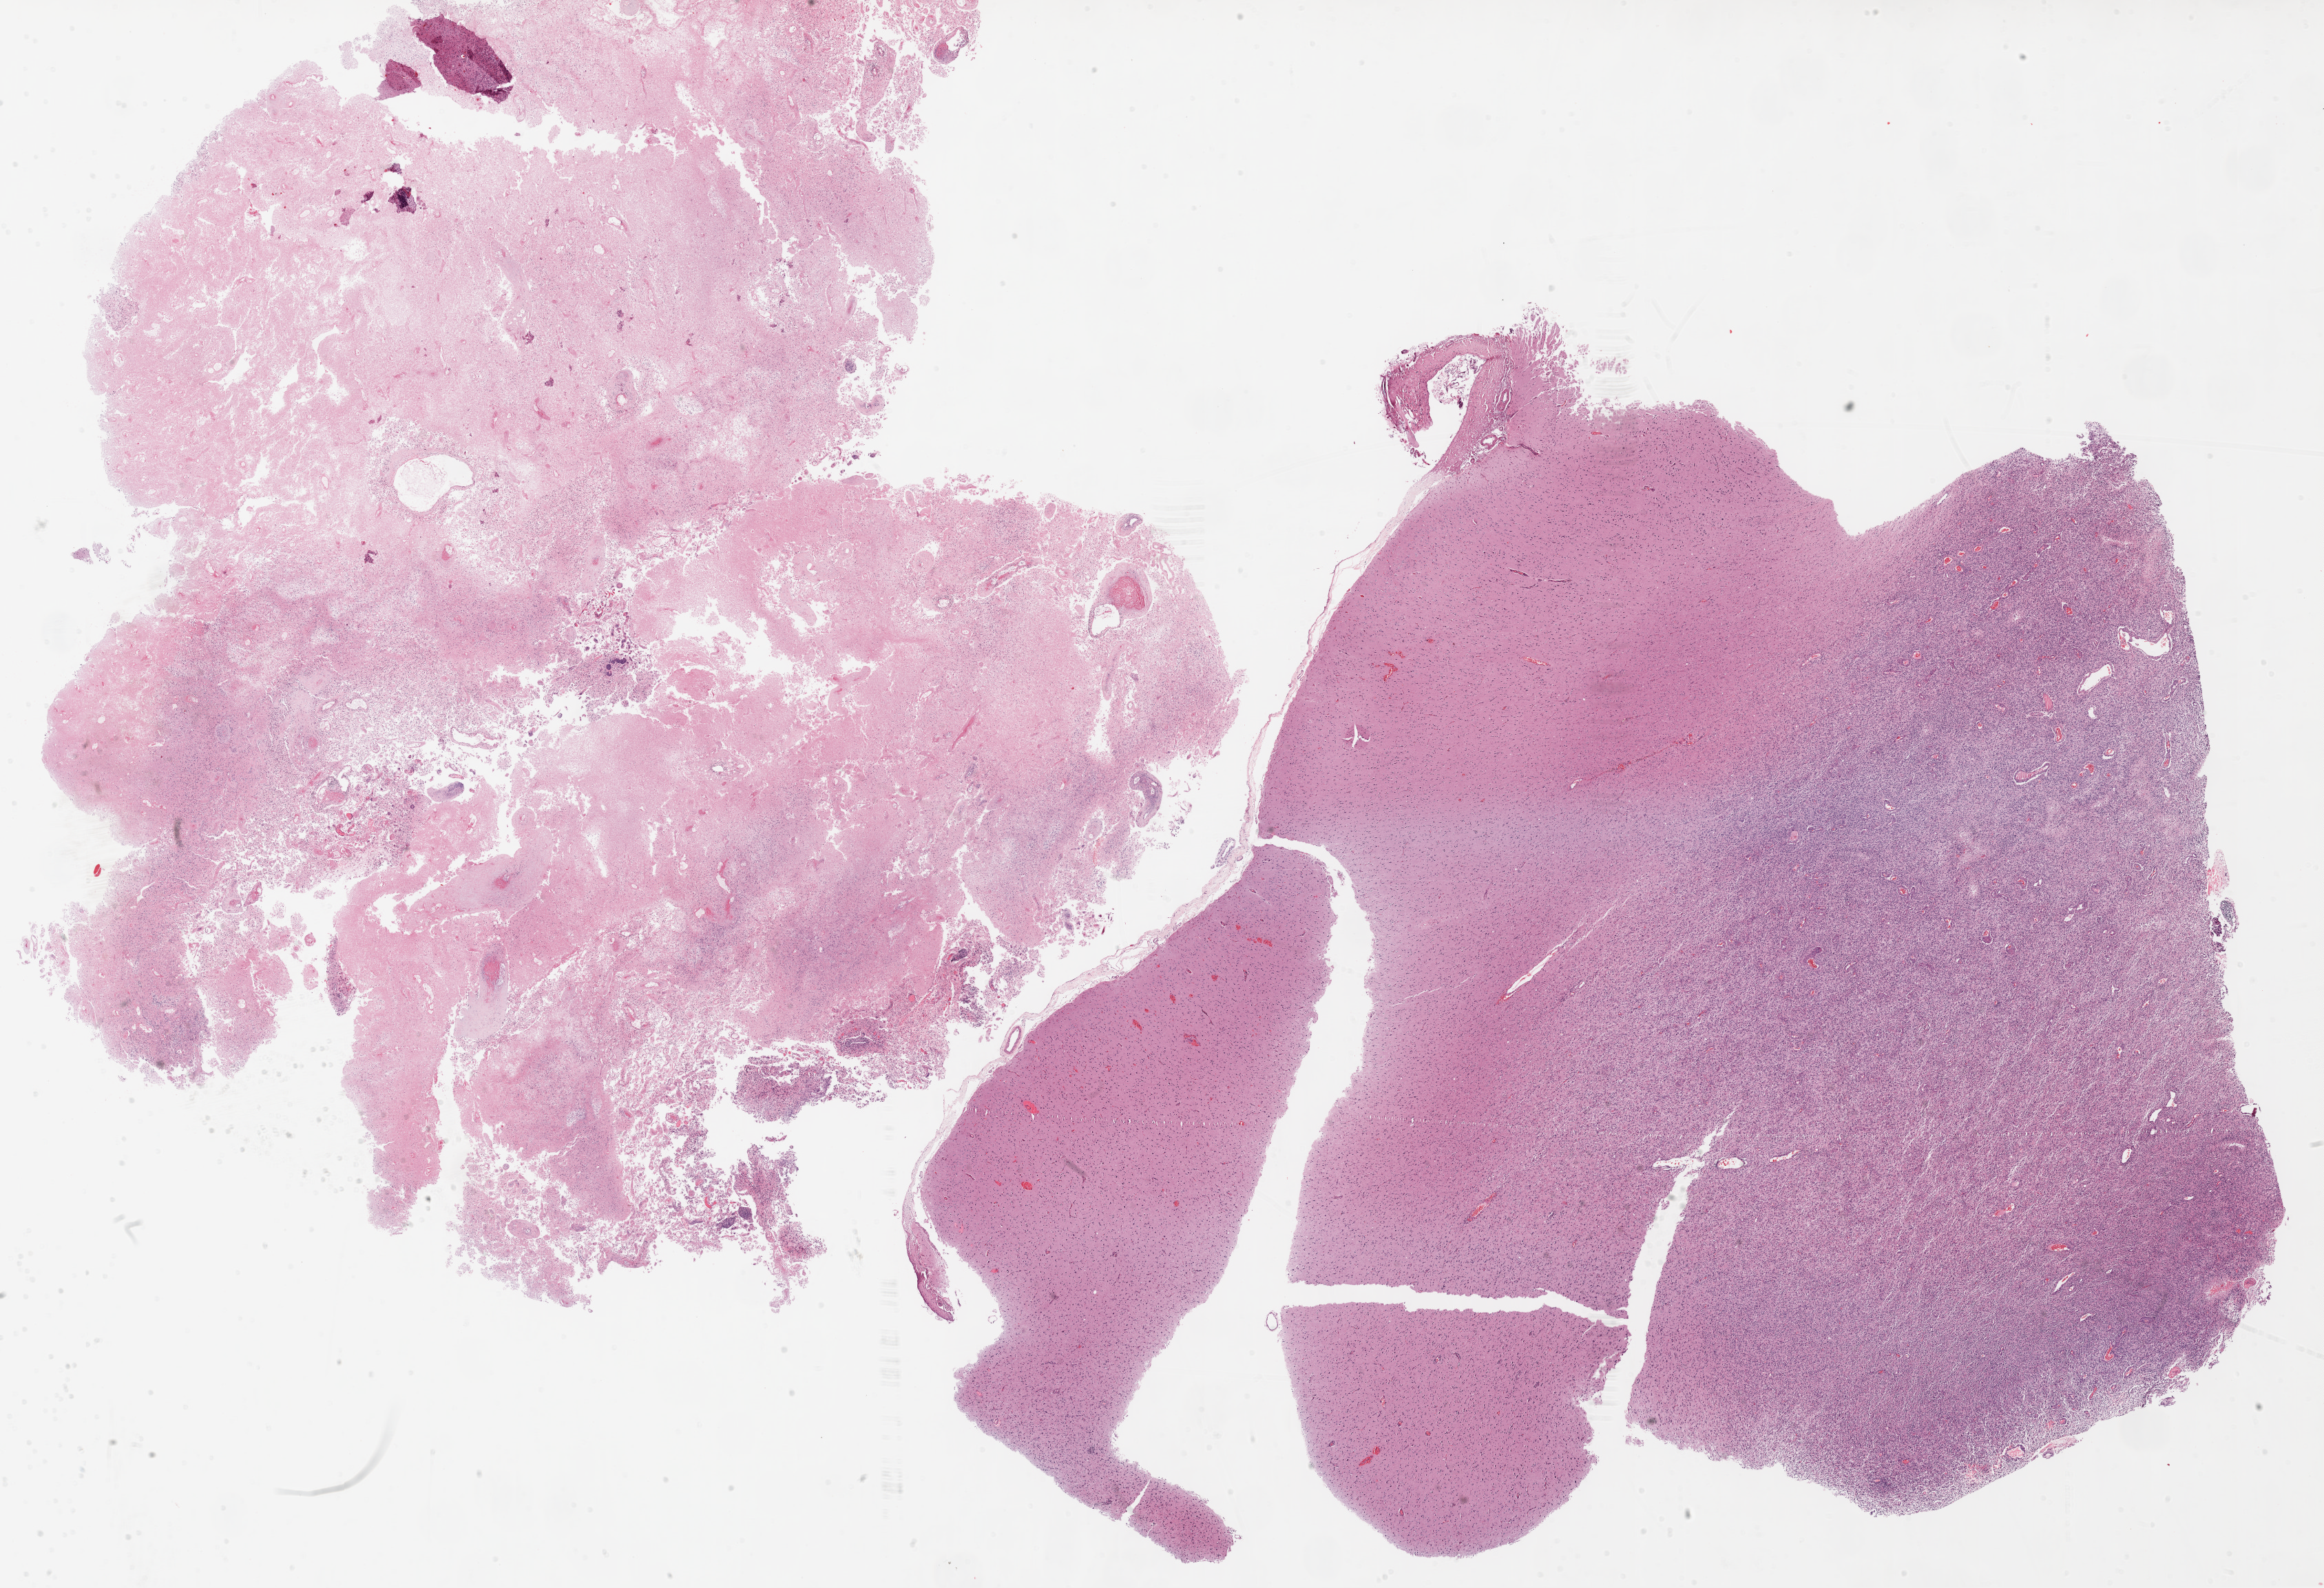
Digitized H&E-stained tissue section (whole slide) — whole scanned area (about 27.1 x 18.5 mm, slide scanned at 20x) shown as a low-resolution overview; FFPE section; brain, primary tumour sample. Male, age 60 years at initial diagnosis.
Pathologic diagnosis: Glioblastoma.